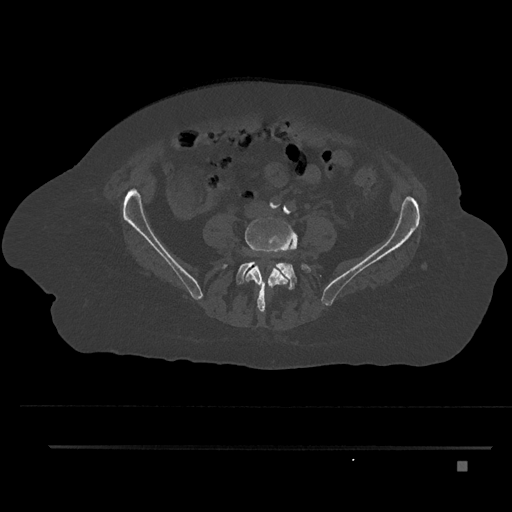
CT including the spine, one axial slice; reconstruction kernel Br40s/3; bone window (W 1800 / L 400 HU); 0.5 mm slice thickness; 512 × 512 image matrix. Female patient, age 76 years. Case-level facts recorded for this patient, not image findings: primary cancer: lung.
Outlined on this slice (semi-automatically segmented with operator editing):
- L4 vertebra: bounding box (x1, y1, x2, y2) in pixels: (245, 217, 297, 313)
- L5 vertebra: (236, 247, 311, 290)